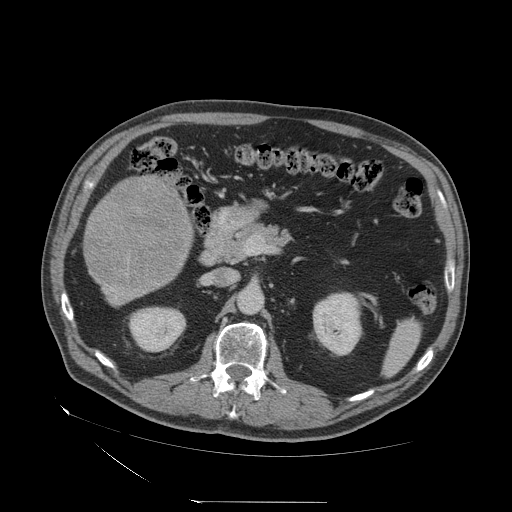
Contrast-enhanced abdominal CT (liver protocol), one axial slice; slice 14 of 83 in the series (ordered by position); soft-tissue window (W 400 / L 40 HU); 2.5 mm slice thickness; 512 × 512 image matrix, field of view 460 × 460 mm. Case-level facts recorded for this patient, not image findings: diagnosis: hepatocellular carcinoma (patient treated with transarterial chemoembolisation; whether this scan precedes or follows treatment is not stated here); TNM stage (as recorded): Stage-I; Child-Pugh class: A; tumour differentiation: well differentiated.
Outlined on this slice (semi-automatic segmentation, software-assisted and operator-edited):
- liver parenchyma outside the tumour (the mass and vessels are separate outlines, so this box may not span the whole liver): bounding box (x1, y1, x2, y2) in pixels: (96, 176, 192, 304)
- mass: (86, 180, 189, 287)